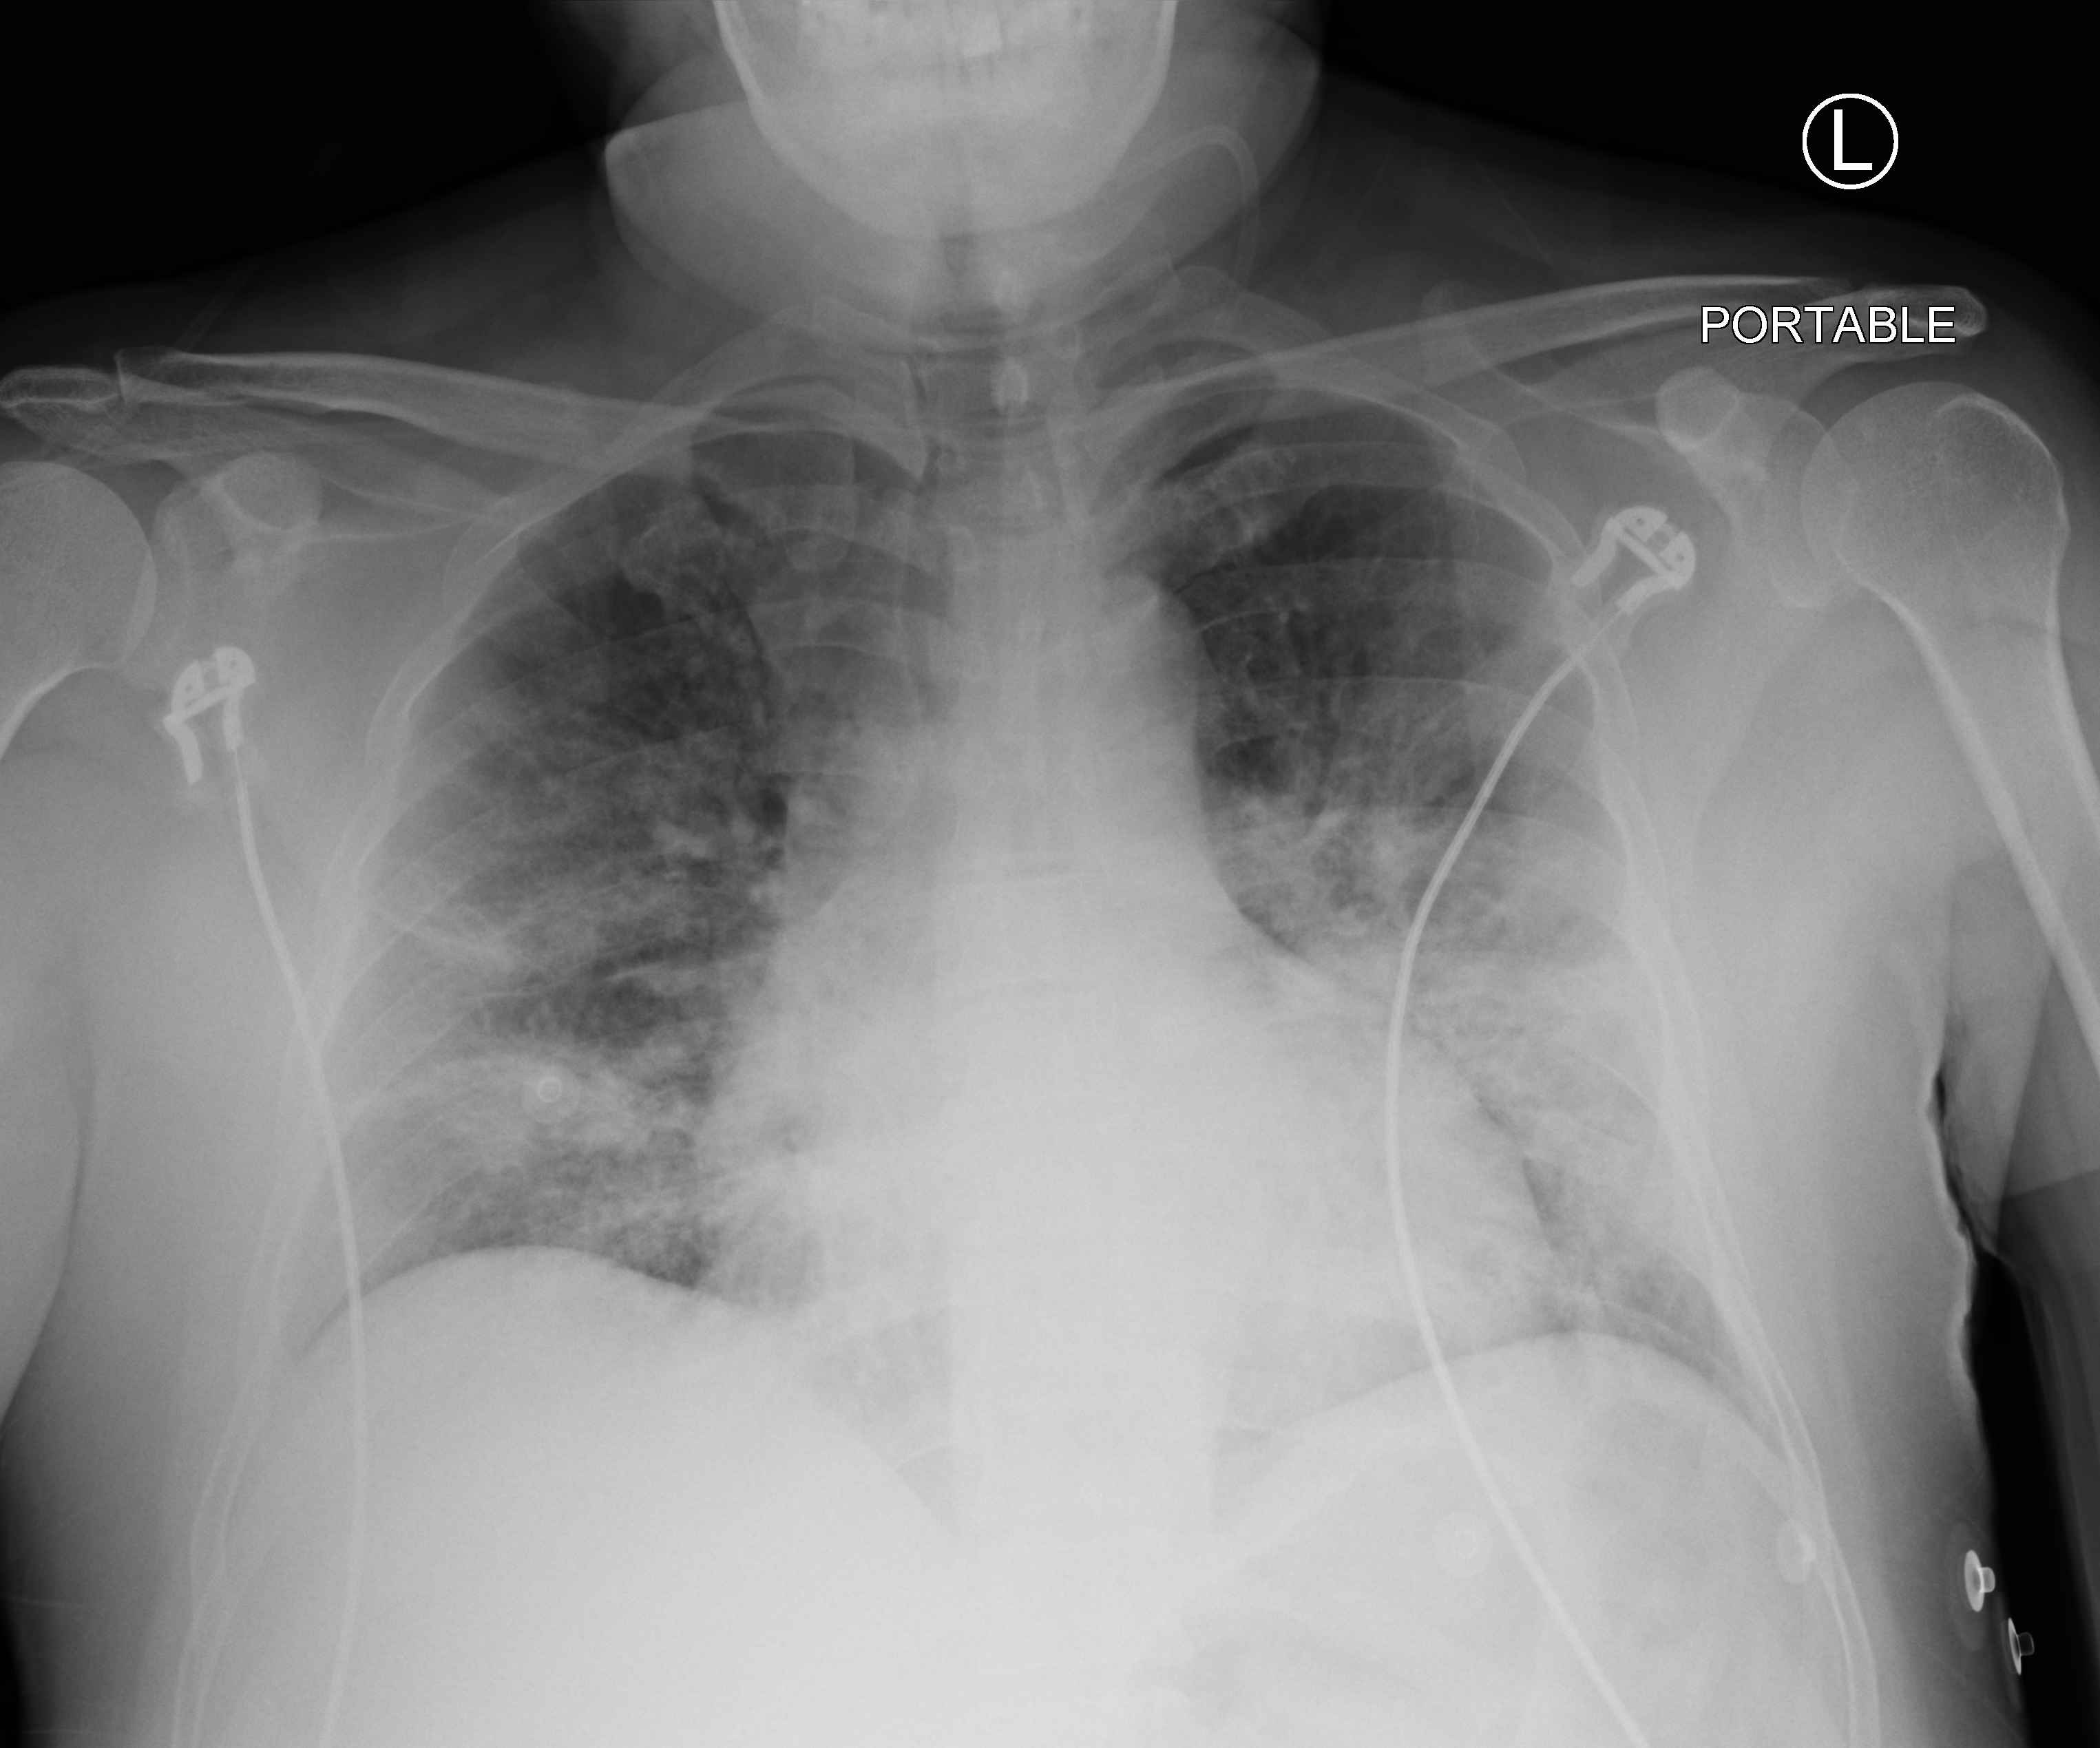
Portable chest radiograph, anteroposterior (AP) projection. Patient hospitalised with COVID-19; male, aged 18–59 years.
From the hospital-stay record, not from the radiograph (when in the stay this image was taken is not recorded): mechanically ventilated during this hospital stay: no; admitted to intensive care during this hospital stay: no.